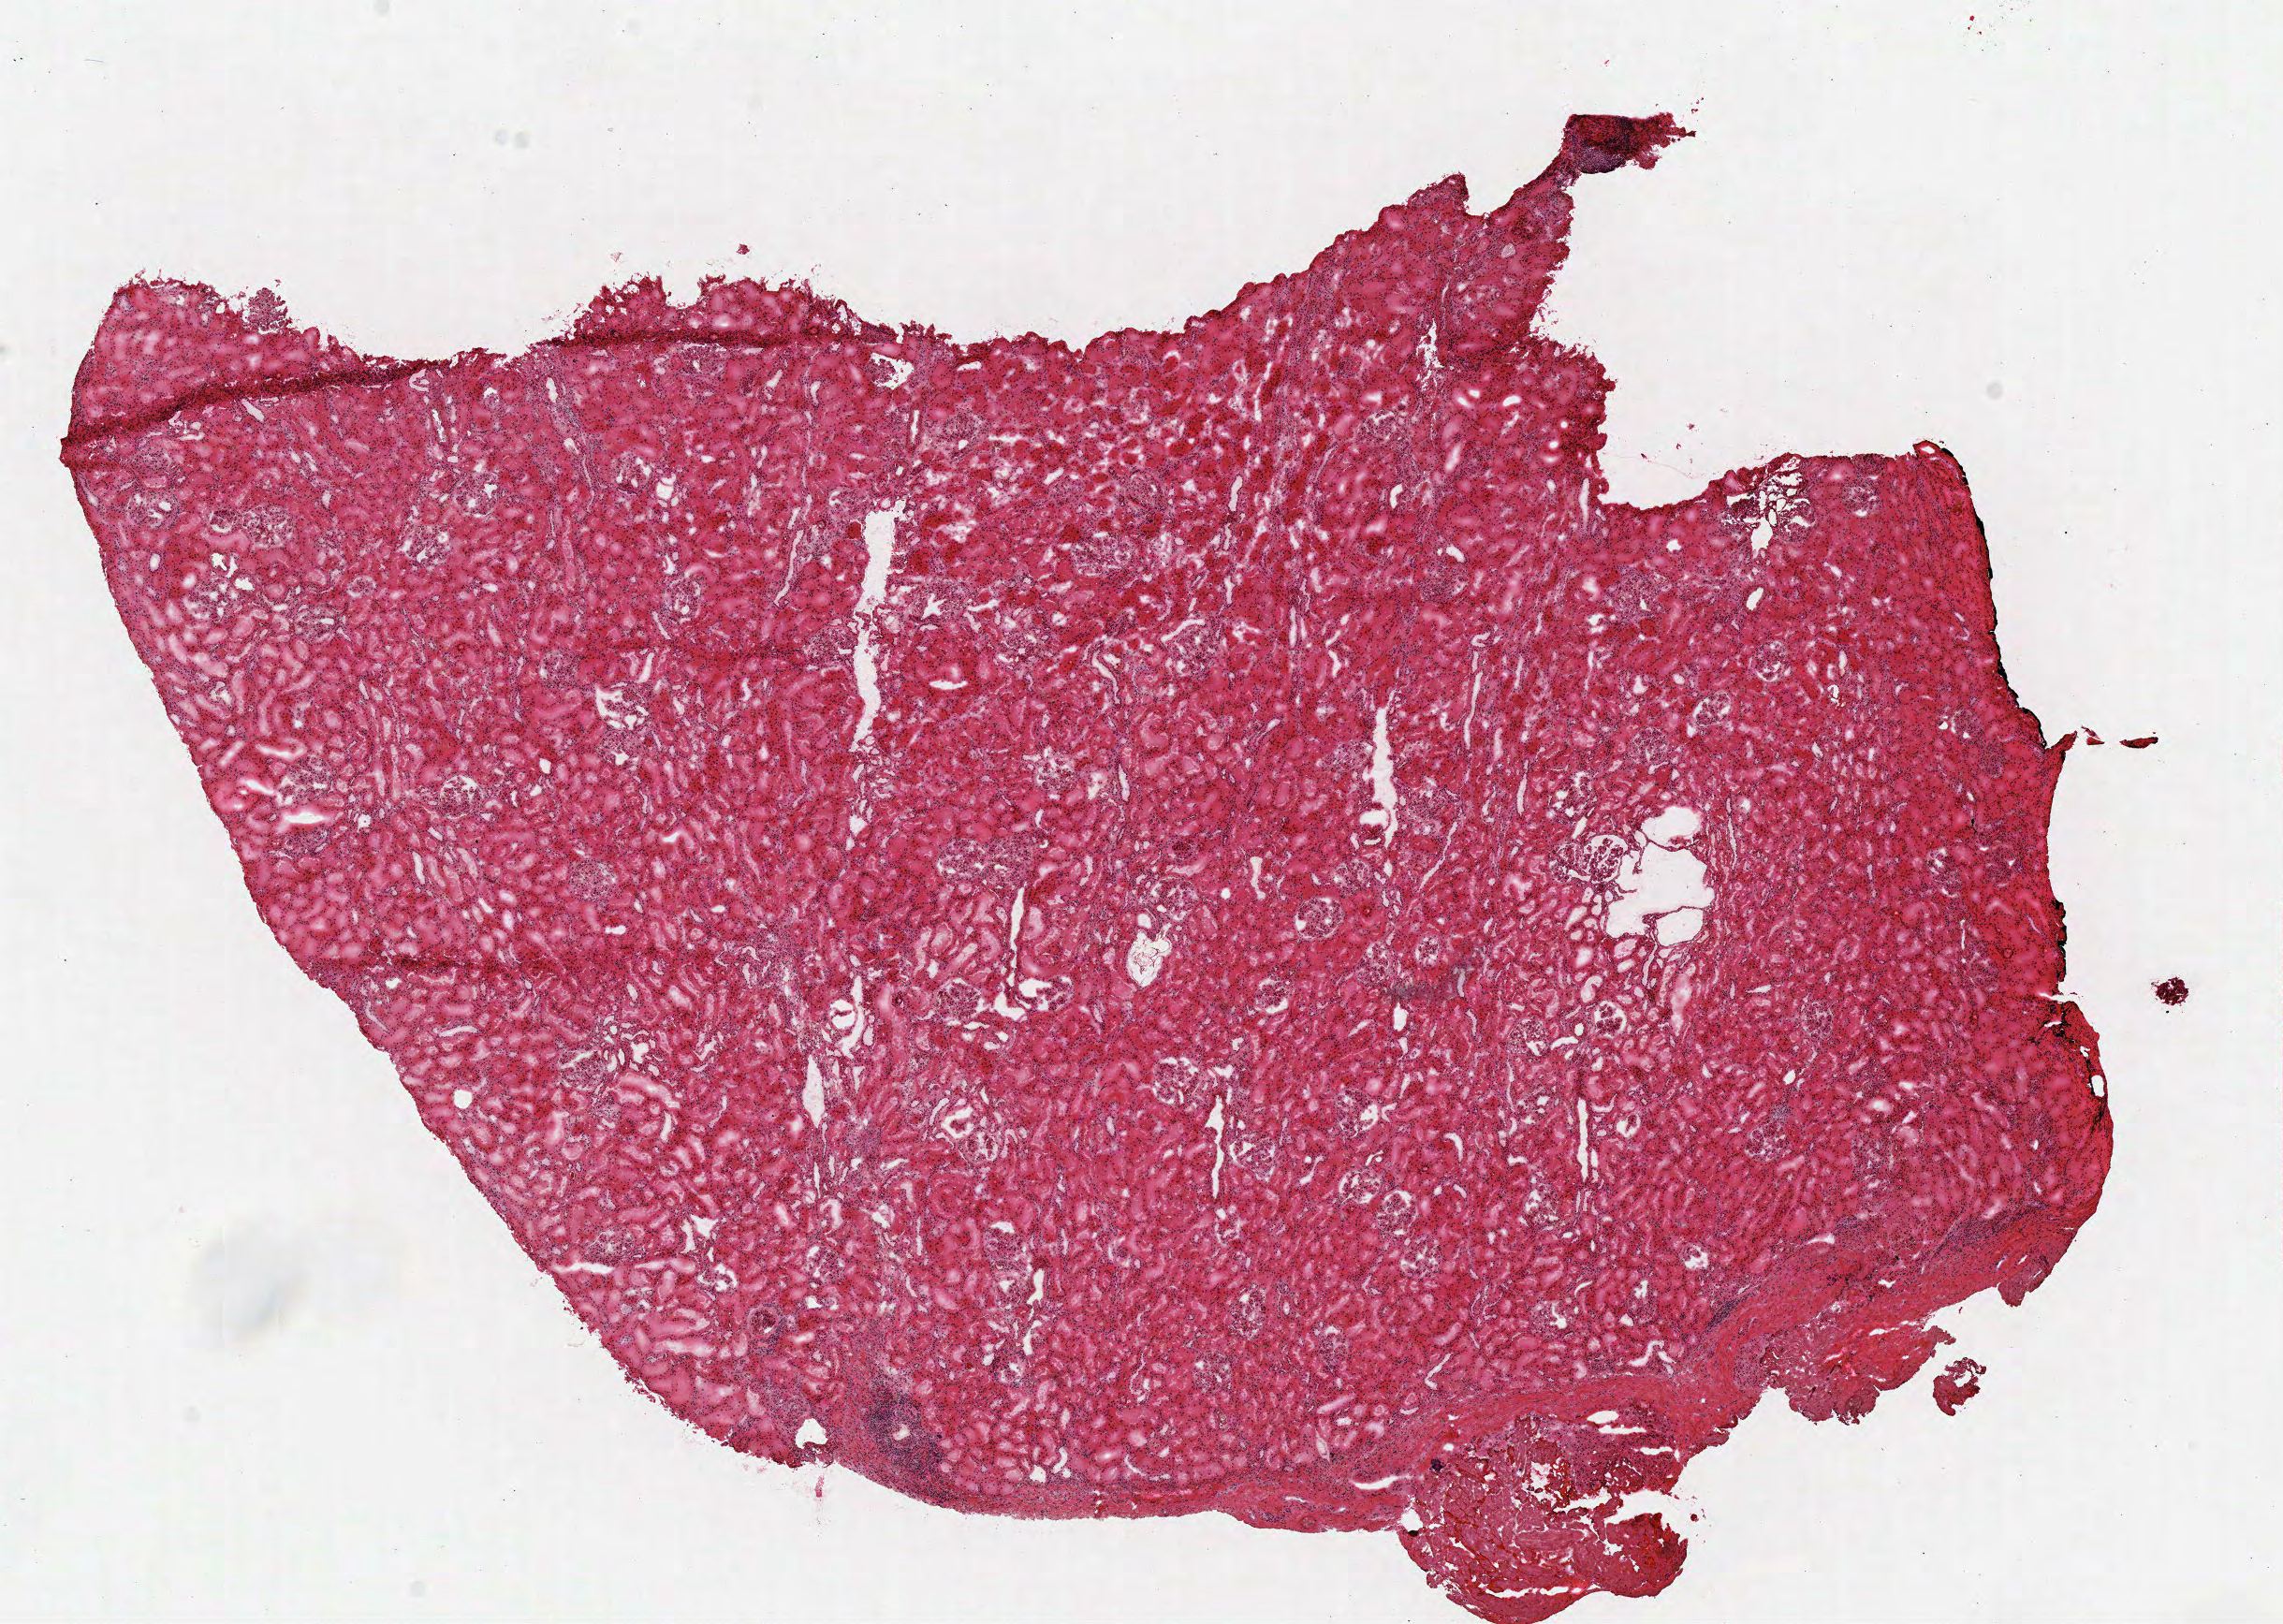
Hematoxylin and eosin (H&E) stained whole-slide image — low-resolution overview of the scanned area, about 9.6 x 6.8 mm (acquisition: 40x scan). Frozen section from the top of the tissue portion. Solid tissue normal (non-tumour tissue) sample from the kidney. Female patient; age at initial diagnosis 59 years.
This section: solid tissue normal sample (biorepository sample class). Patient diagnosis: Papillary adenocarcinoma, NOS.